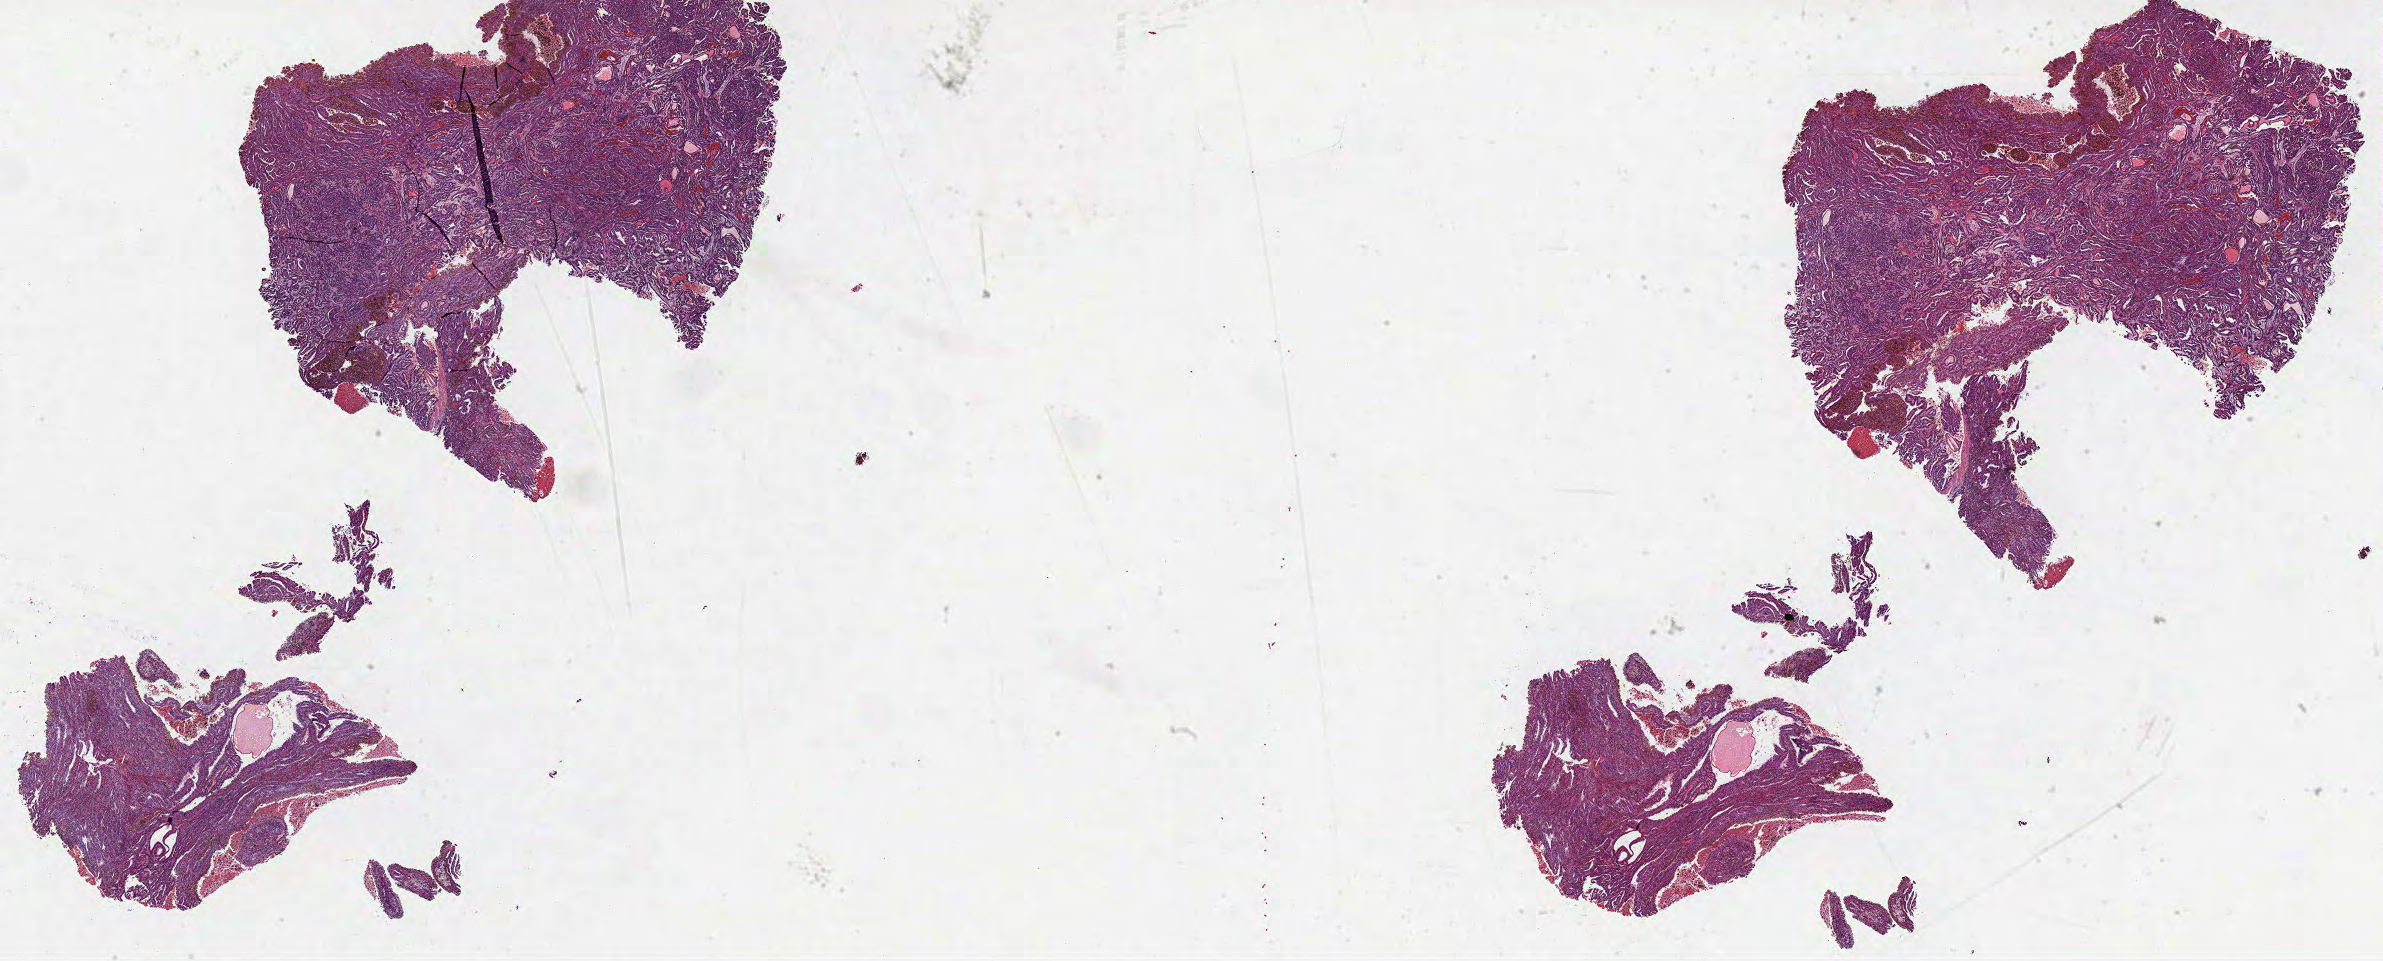
Whole-slide histology image, H&E-stained — low-resolution overview of the scanned area, about 38.4 x 15.5 mm (from a 40x scan). Formalin-fixed paraffin-embedded (FFPE) diagnostic section. Sample: primary tumour, kidney. Patient: male, age at initial diagnosis 56 years.
• pathologic diagnosis: Papillary adenocarcinoma, NOS
• AJCC pathologic stage: I
• TNM: T1a NX M0